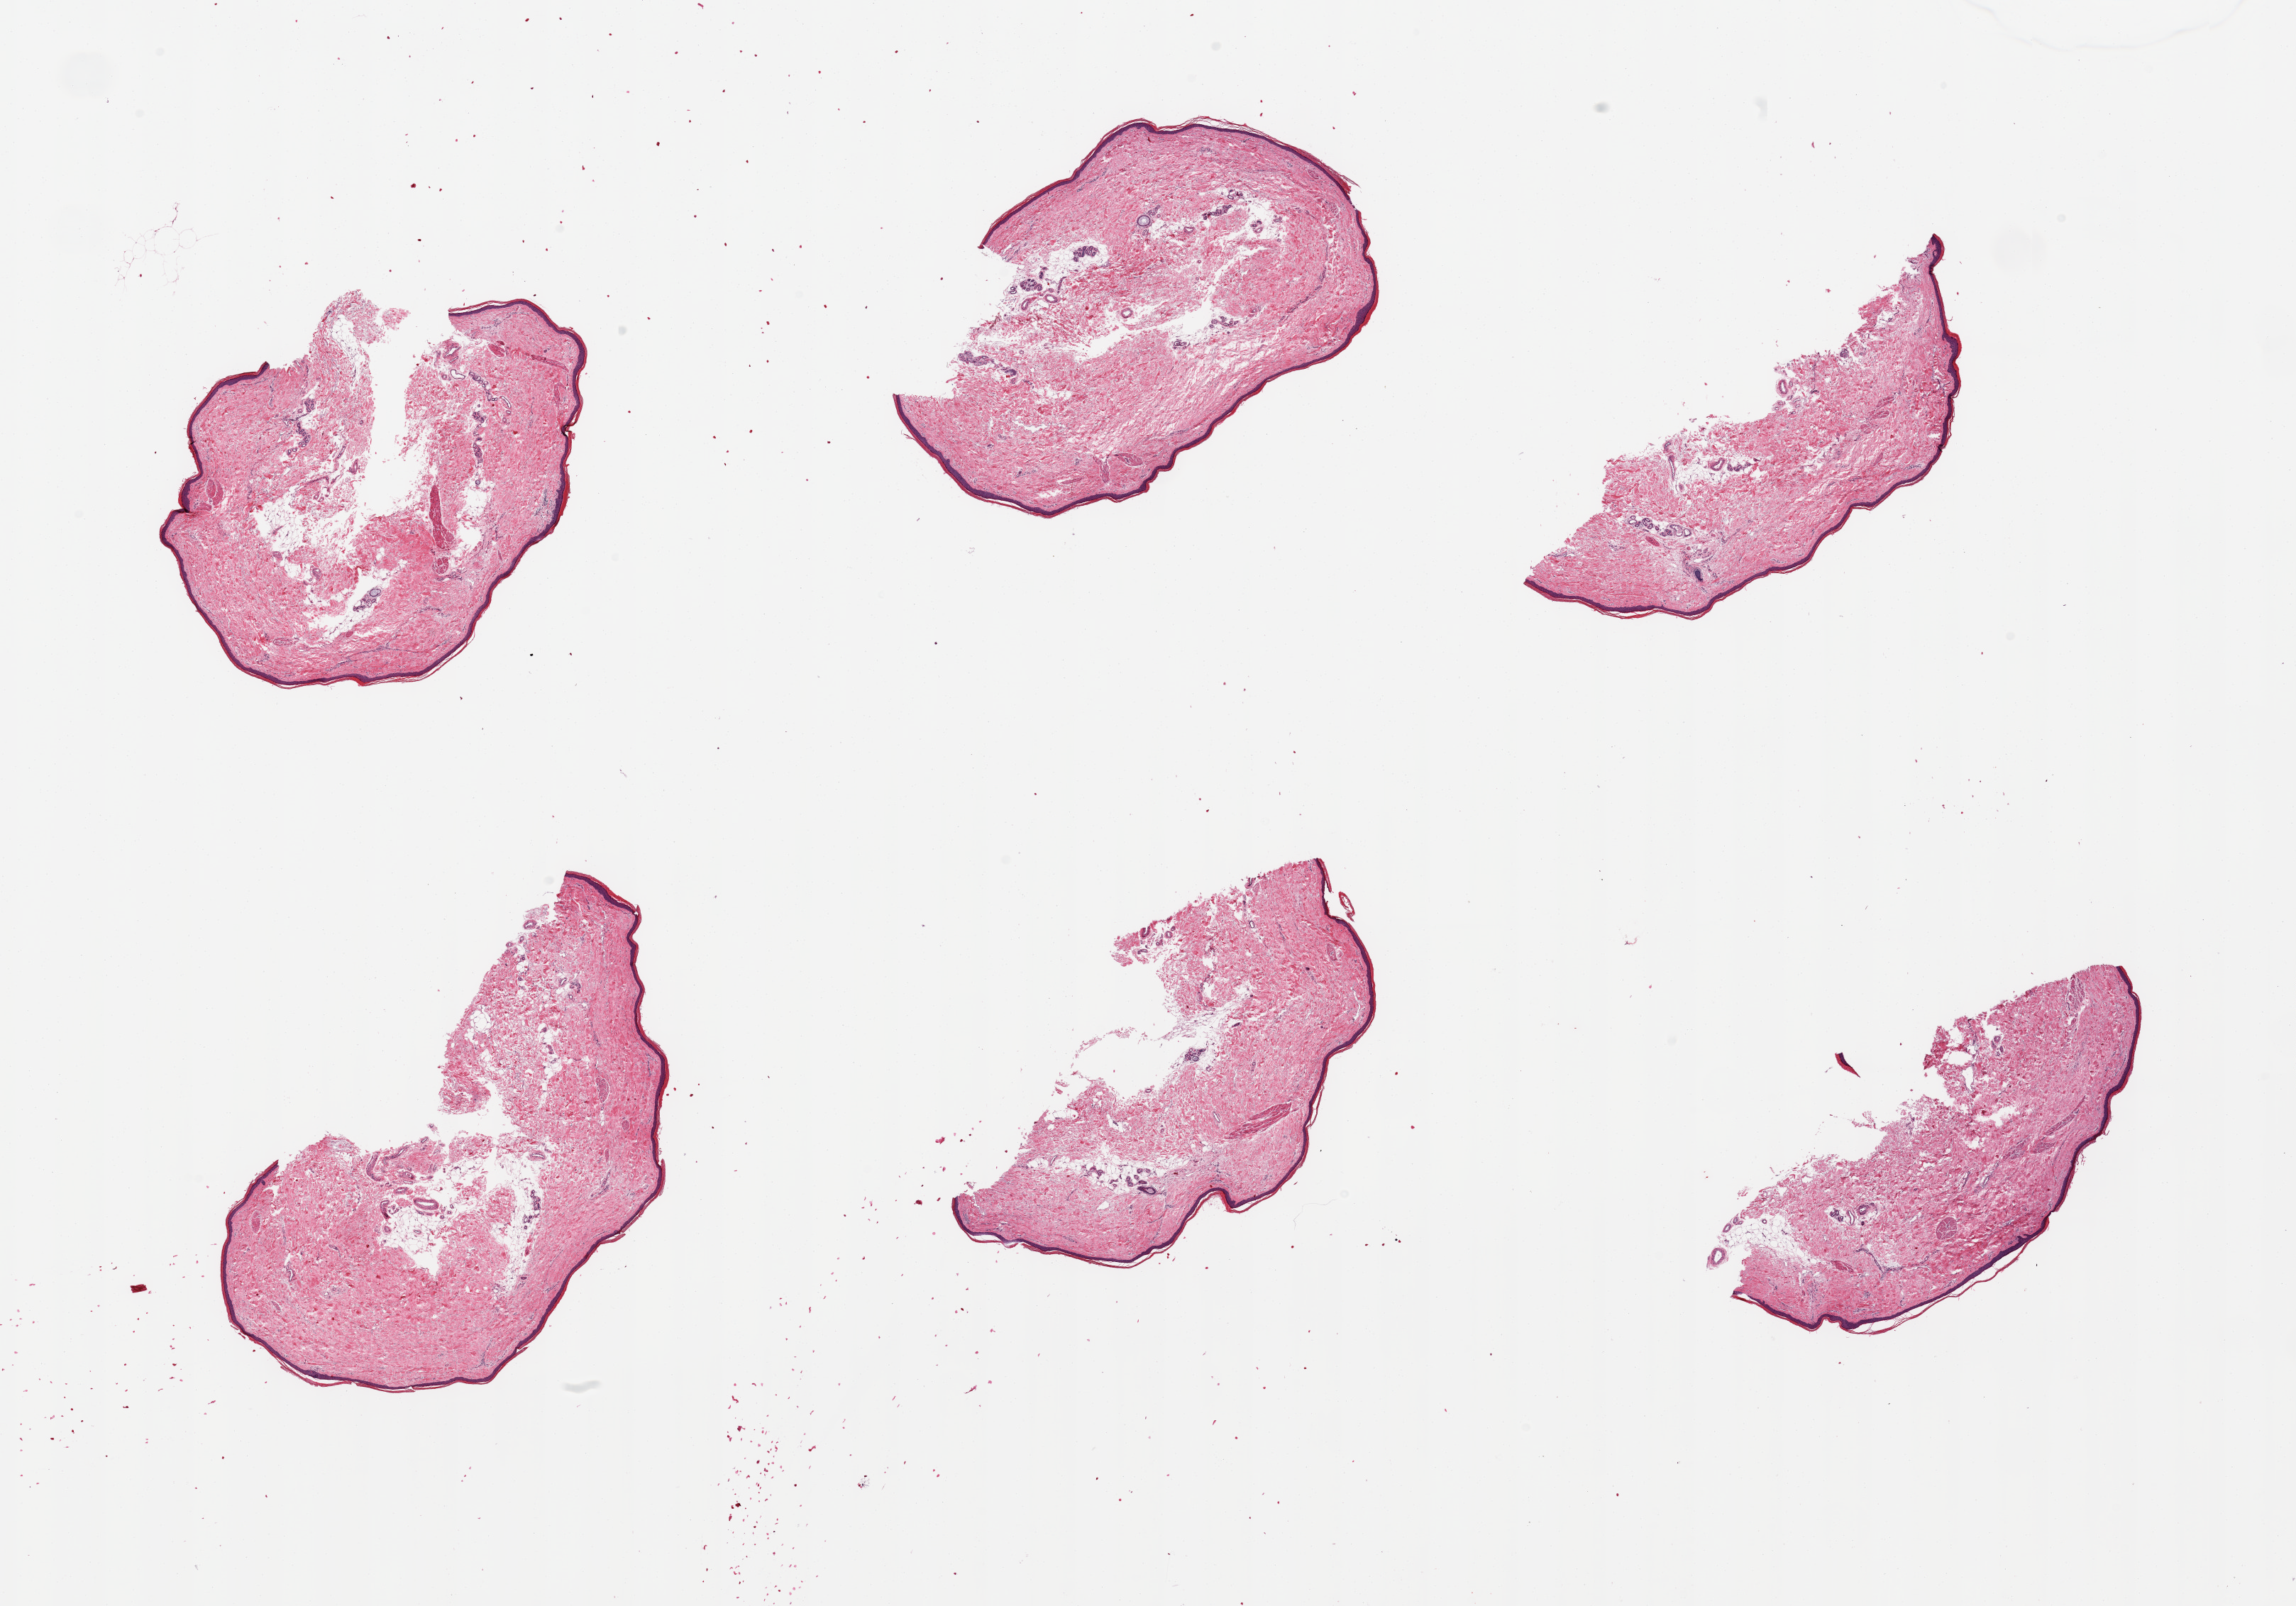
Whole-slide image, H&E stain, whole scanned area (about 25.6 x 17.9 mm) shown as a low-resolution overview; PAXgene-fixed paraffin-embedded (PFPE) section; sampled site (target tissue): skin of lower leg; tissue donor sample. Donor sex: female.
Reviewer comment on this tissue sample: 6 pieces, minimal dermal fat; squamous epithelium is ~45 microns.